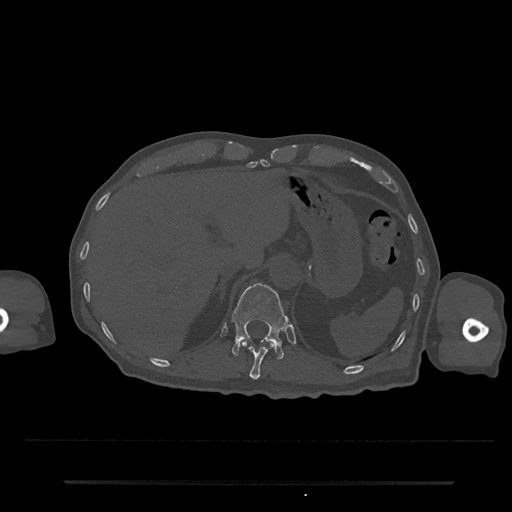
CT including the spine, one axial slice. Slice 220 of 797 in the series (ordered by position). 120 kVp. Bone window (W 1800 / L 400 HU). 512 × 512 image matrix. Patient: male, 74 years. Case-level facts recorded for this patient, not image findings: primary cancer: prostate.
Structures marked on this image (semi-automatic segmentation, software-assisted and operator-edited):
- T11 vertebra: box from (x=241, y=340) to (x=274, y=380) px
- T12 vertebra: (x=231, y=283)–(x=289, y=359)